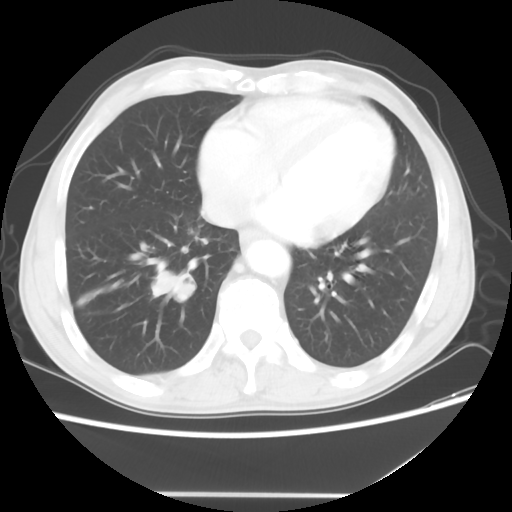
Chest CT, one axial slice. Slice 16 of 56 in the series (ordered by position). Reconstruction kernel STANDARD. 120 kVp. Lung window (W 1500 / L -600 HU). 5 mm slice thickness. 512 × 512 image matrix. Male patient, age 65 years. Case-level facts recorded for this patient, not image findings: clinical TNM (as recorded): T1c N3 M0; histopathological grade: G3.
Structures marked on this image (rectangle marked by the reading radiologist):
- lung tumour (recorded histology: small cell carcinoma): bounding box (x1, y1, x2, y2) in pixels: (141, 252, 202, 303)